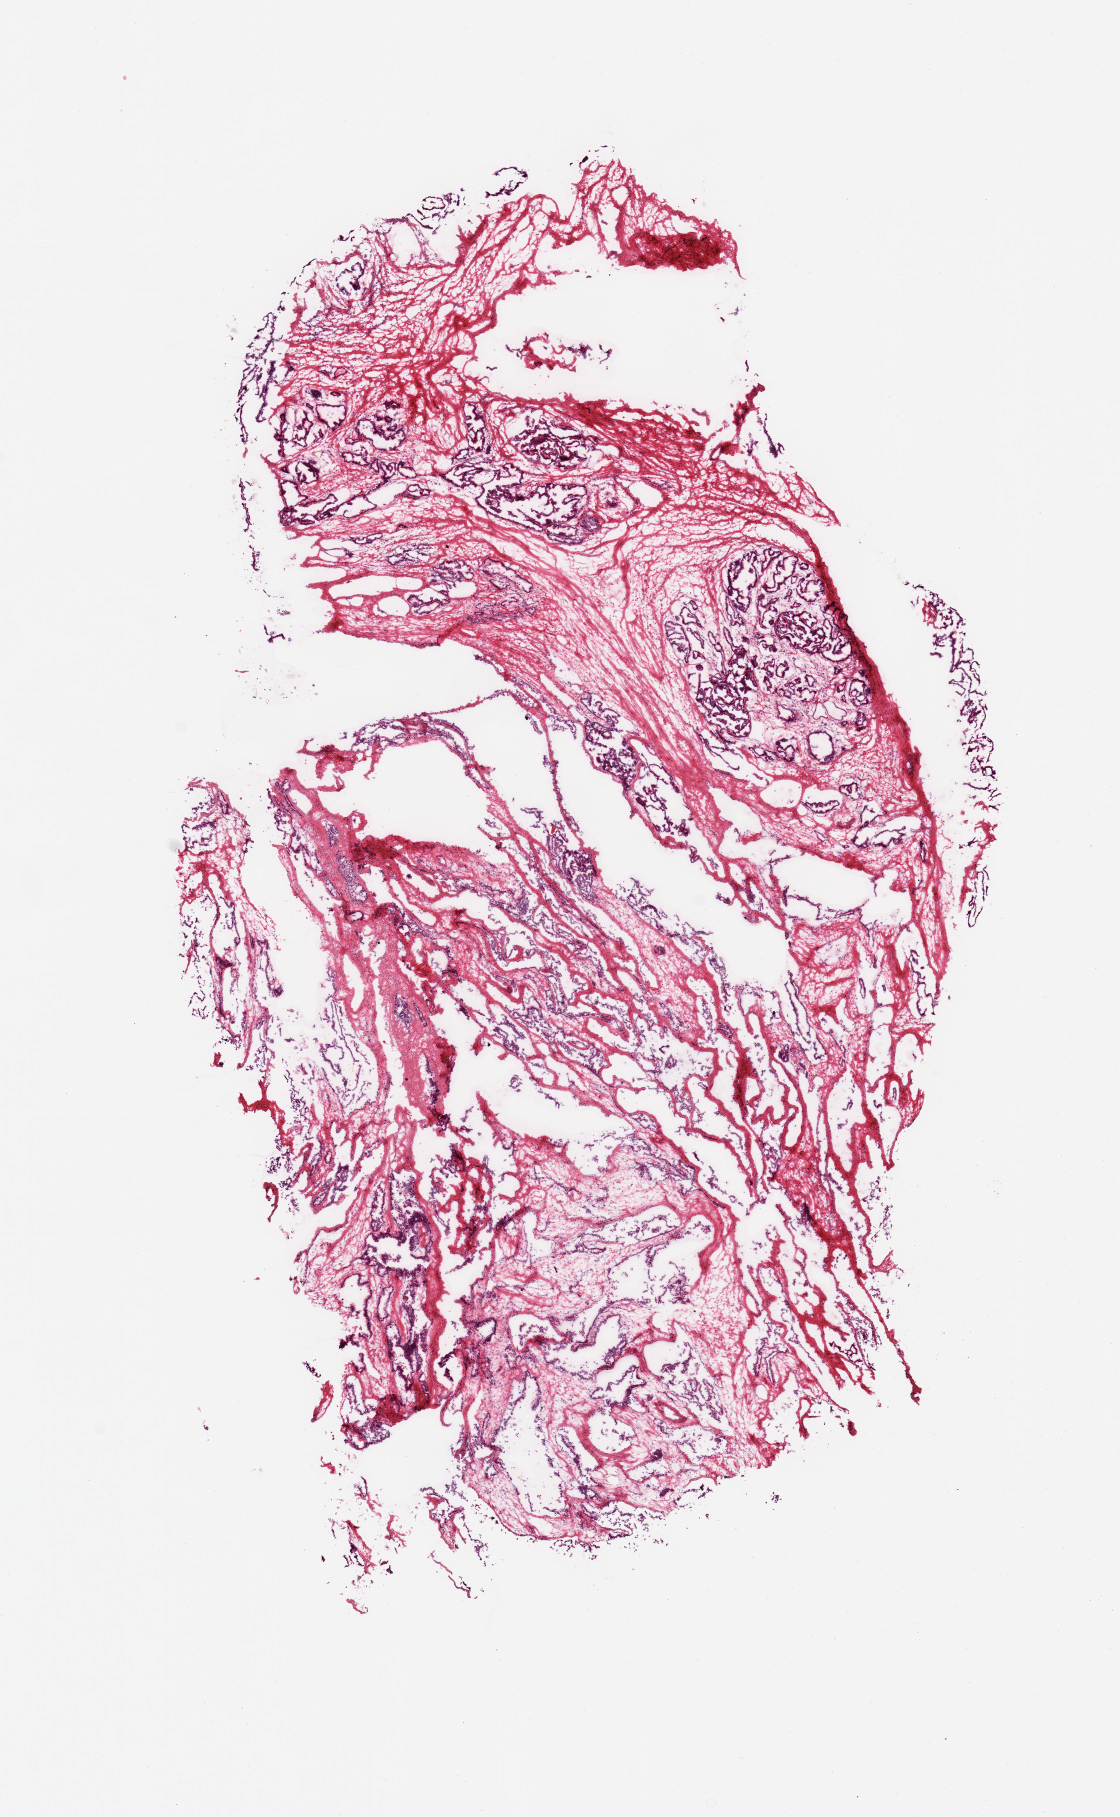
Digitized haematoxylin and eosin-stained section — shown as a low-resolution overview of the whole scanned area (about 8.9 x 14.4 mm, slide scanned at 20x). Donor sex: male.
- specimen: frozen section; target tissue: prostate; donor tissue sample